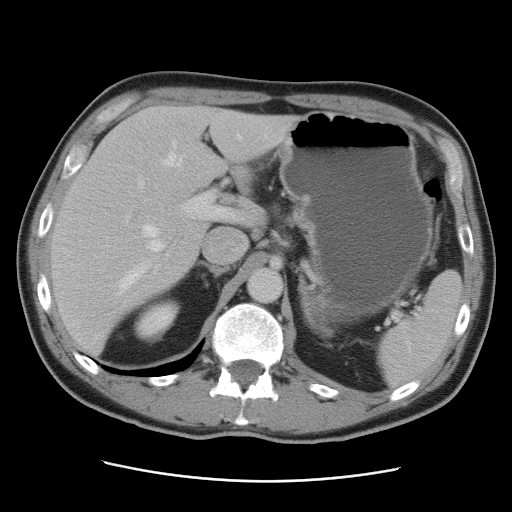
Contrast-enhanced abdominal CT, one axial slice; slice 58 of 89 in the series (ordered by position); 120 kVp; intravenous contrast given; soft-tissue window (W 400 / L 40 HU); 5 mm slice thickness; 512 × 512 image matrix. Male patient, age 59 years. Case-level facts recorded for this patient, not image findings: diagnosis: colorectal cancer liver metastases, imaged before liver resection; multiple liver metastases: yes; largest metastasis: 0.6 cm; disease in both lobes: yes.
Outlined on this slice (manually delineated by an expert):
- hepatic veins: bounding box (x1, y1, x2, y2) in pixels: (116, 135, 266, 303)
- liver: (51, 105, 296, 355)
- planned liver remnant (the part of the liver to remain after resection): (77, 106, 258, 238)
- portal vein (with intrahepatic branches): (126, 180, 235, 271)